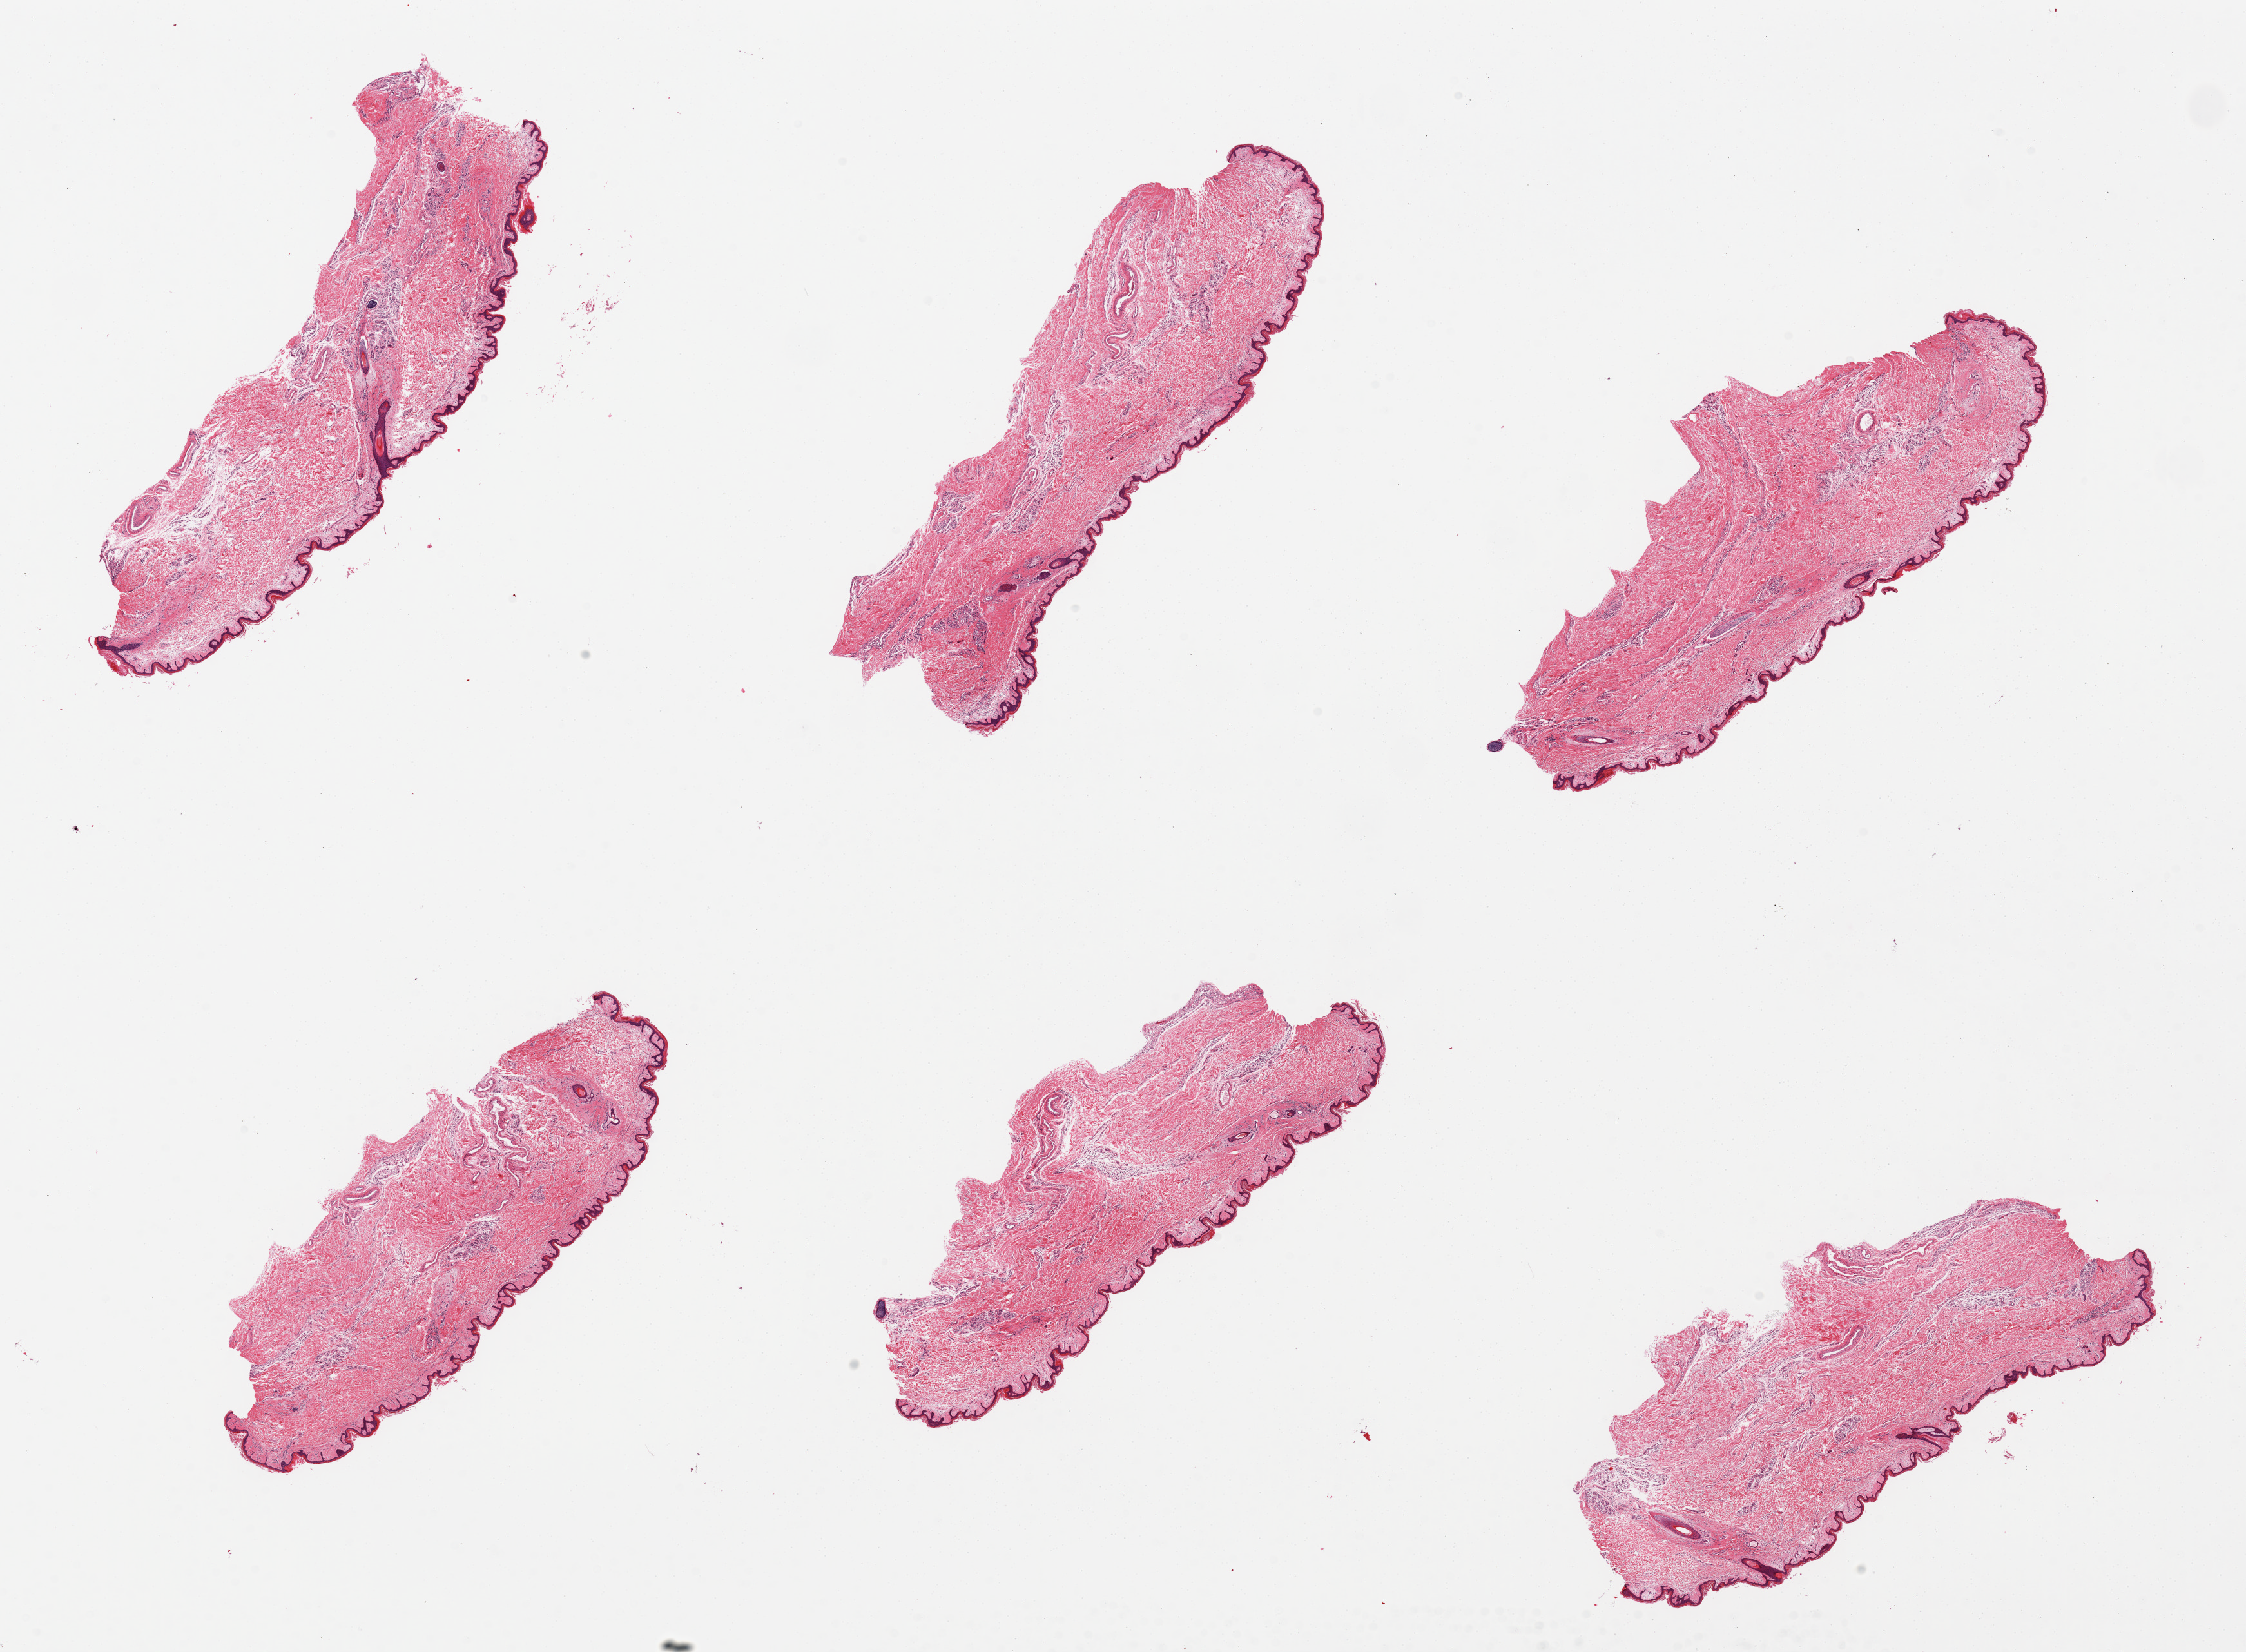
Hematoxylin and eosin (H&E) whole-slide image, brightfield, whole scanned area (about 27.6 x 20.3 mm, acquisition: 20x scan) shown as a low-resolution overview. PAXgene-fixed paraffin-embedded (PFPE) section. Section of skin of suprapubic region (target tissue). Donor tissue sample. Donor: male.
Reviewer comment on this tissue sample: 6 pieces; squamous epithelium is ~1-1.5% thickness, ~30 microns.